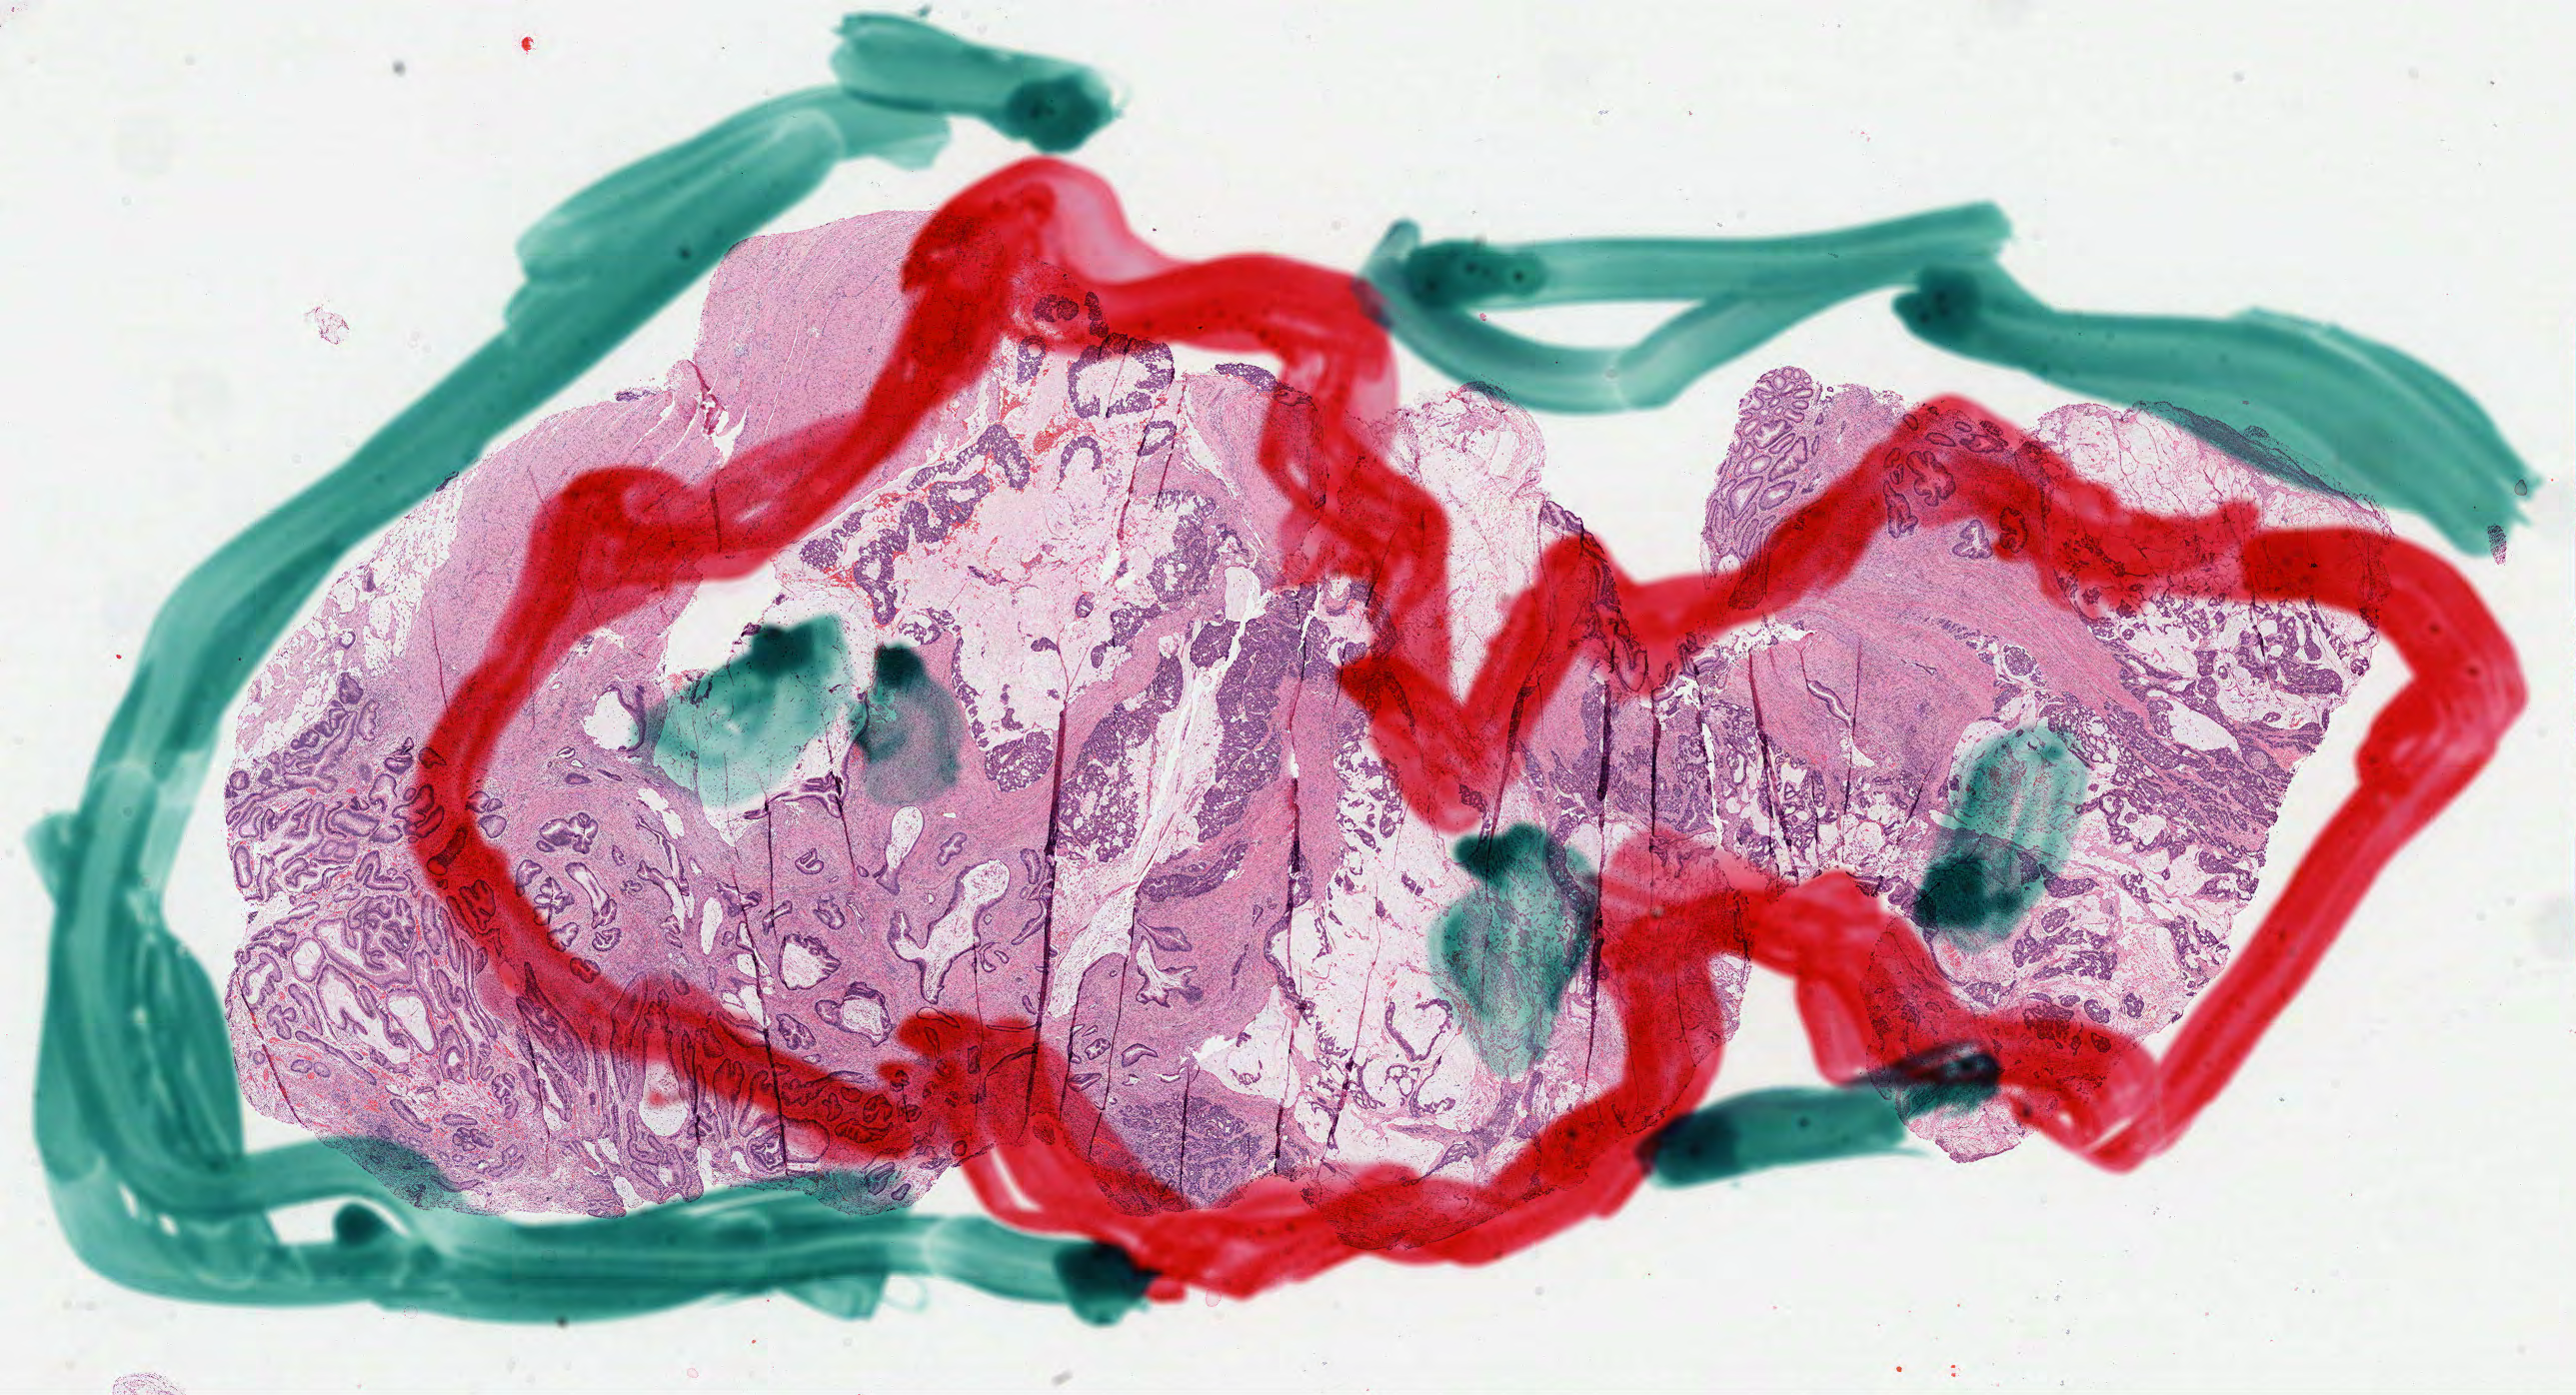
Digitized Hematoxylin and eosin (H&E) stained tissue section (whole slide) — a low-resolution overview of the entire scanned area, about 20.8 x 11.3 mm (acquisition: 40x scan); formalin-fixed paraffin-embedded (FFPE) diagnostic section; primary tumour sample from the colon. Male, age 60 years at initial diagnosis.
Pathologic diagnosis: Mucinous adenocarcinoma (sigmoid colon). AJCC pathologic stage: IIIC.